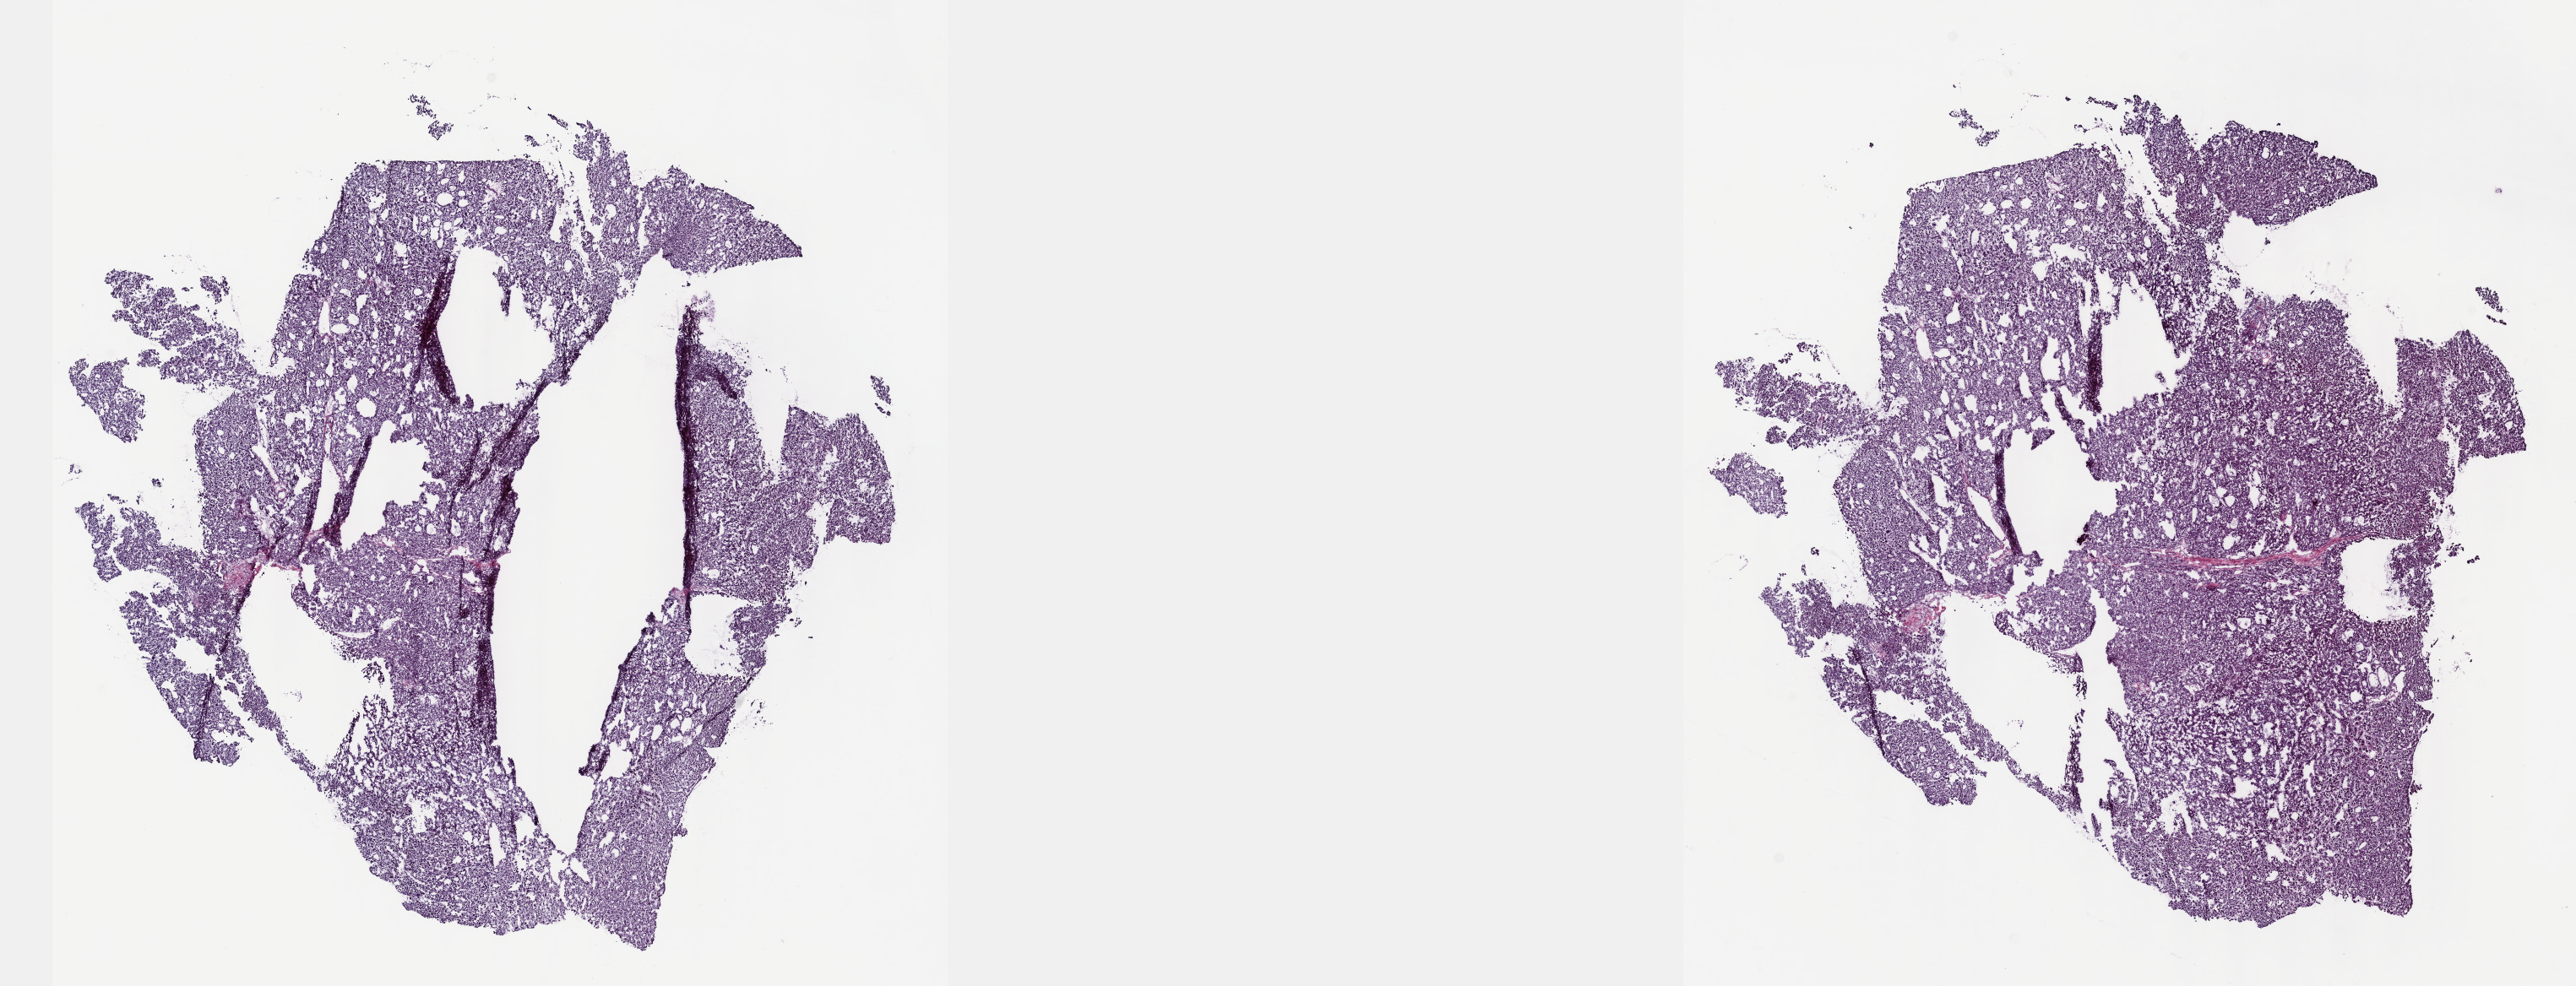
Whole-slide histology image, H&E-stained, low-resolution overview of the scanned area, about 24.6 x 9.4 mm (slide scanned at 40x); frozen section from the top of the tissue portion; sample: primary tumour, liver. Male, age 55 years at initial diagnosis. Histologic grade: G2 (moderately differentiated). Slide review estimates, as recorded: tumour cells 85%, tumour nuclei 85%, normal cells 0%, stromal cells 15%, necrosis 0%. Inflammatory infiltration, as recorded: lymphocyte infiltration 2%, monocyte infiltration 1%, neutrophil infiltration 3%.
* TNM: T3 N0 M0
* histologic diagnosis: Hepatocellular carcinoma, NOS
* AJCC pathologic stage: IIIA (6th edition)